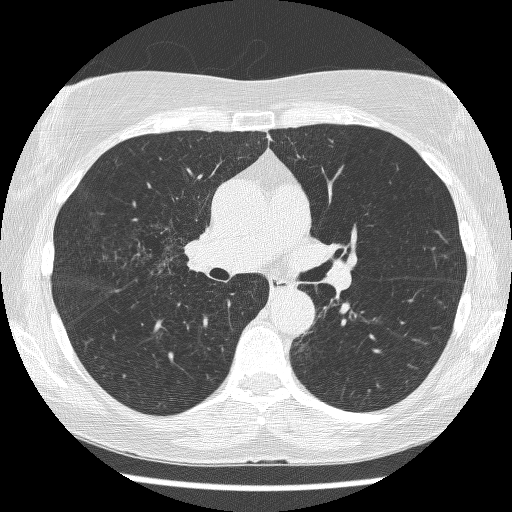
Chest CT (low-dose screening protocol), one axial image; first (baseline) screen; lung window (W 1500 / L -600 HU); 1.25 mm slice thickness; slice 162 of 271 in the series; 512 × 512 image matrix, field of view 316 × 316 mm. Female, age 64 years at enrolment. Former smoker at enrolment.
Expert reader's lesion annotation, bounding box (x1, y1, x2, y2) in pixels: (122, 213, 198, 272). The screening reader recorded 3 non-calcified nodules or masses ≥4 mm on this exam (right upper lobe, right upper lobe, left lower lobe); which of them this box marks is not recorded. Later outcome: lung cancer diagnosed 735 days after this screen (after the third annual screen) — adenocarcinoma, NOS, right upper lobe, right middle lobe, right hilum, stage IV (AJCC 6th edition), 85 mm at pathology.